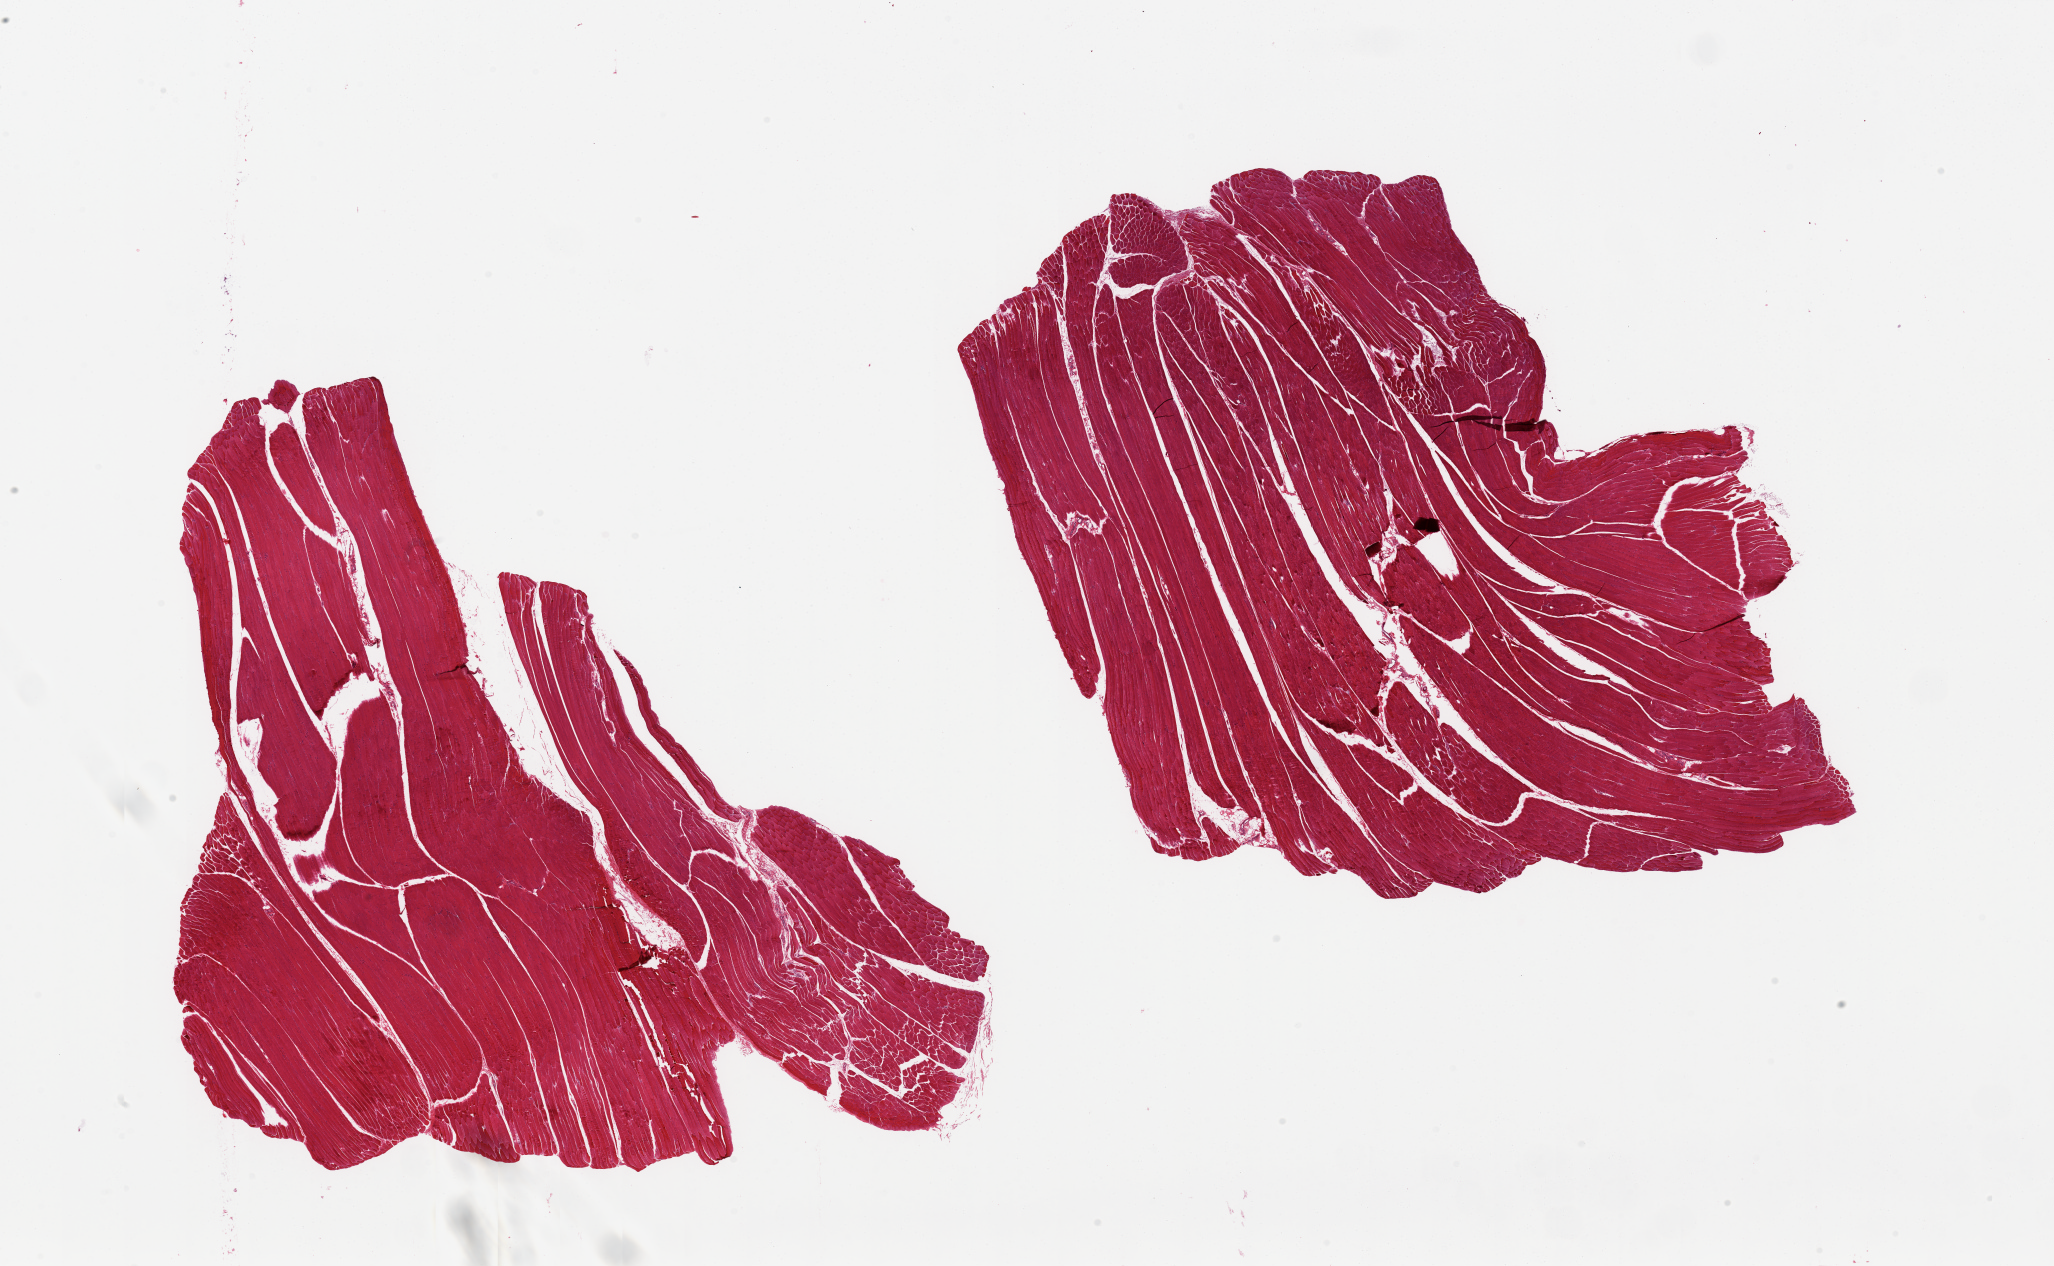
Haematoxylin and eosin whole-slide image, brightfield — a low-resolution overview of the entire scanned area, about 32.5 x 20.0 mm. PAXgene-fixed, paraffin-embedded tissue. Section of skeletal muscle (target tissue). Tissue donor sample.
Pathologist's review note for this sample: 2 pieces, minimal interstitial fat.